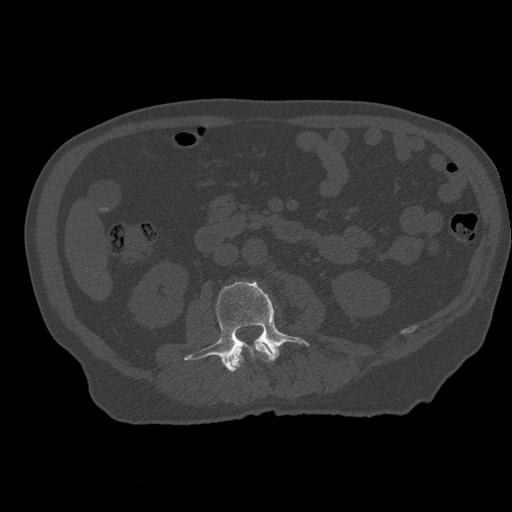
CT including the spine, one axial slice. Position 194 of 399 along the scan axis. Bone window (W 1800 / L 400 HU). 512 × 512 image matrix, field of view 407 × 407 mm. Patient age 73 years. From the clinical record (not read from this slice): primary cancer: prostate.
Outlined on this slice (semi-automatic segmentation, software-assisted and operator-edited):
- L2 vertebra: box from (x=231, y=342) to (x=273, y=371) px
- L3 vertebra: (x=184, y=281)–(x=309, y=372)